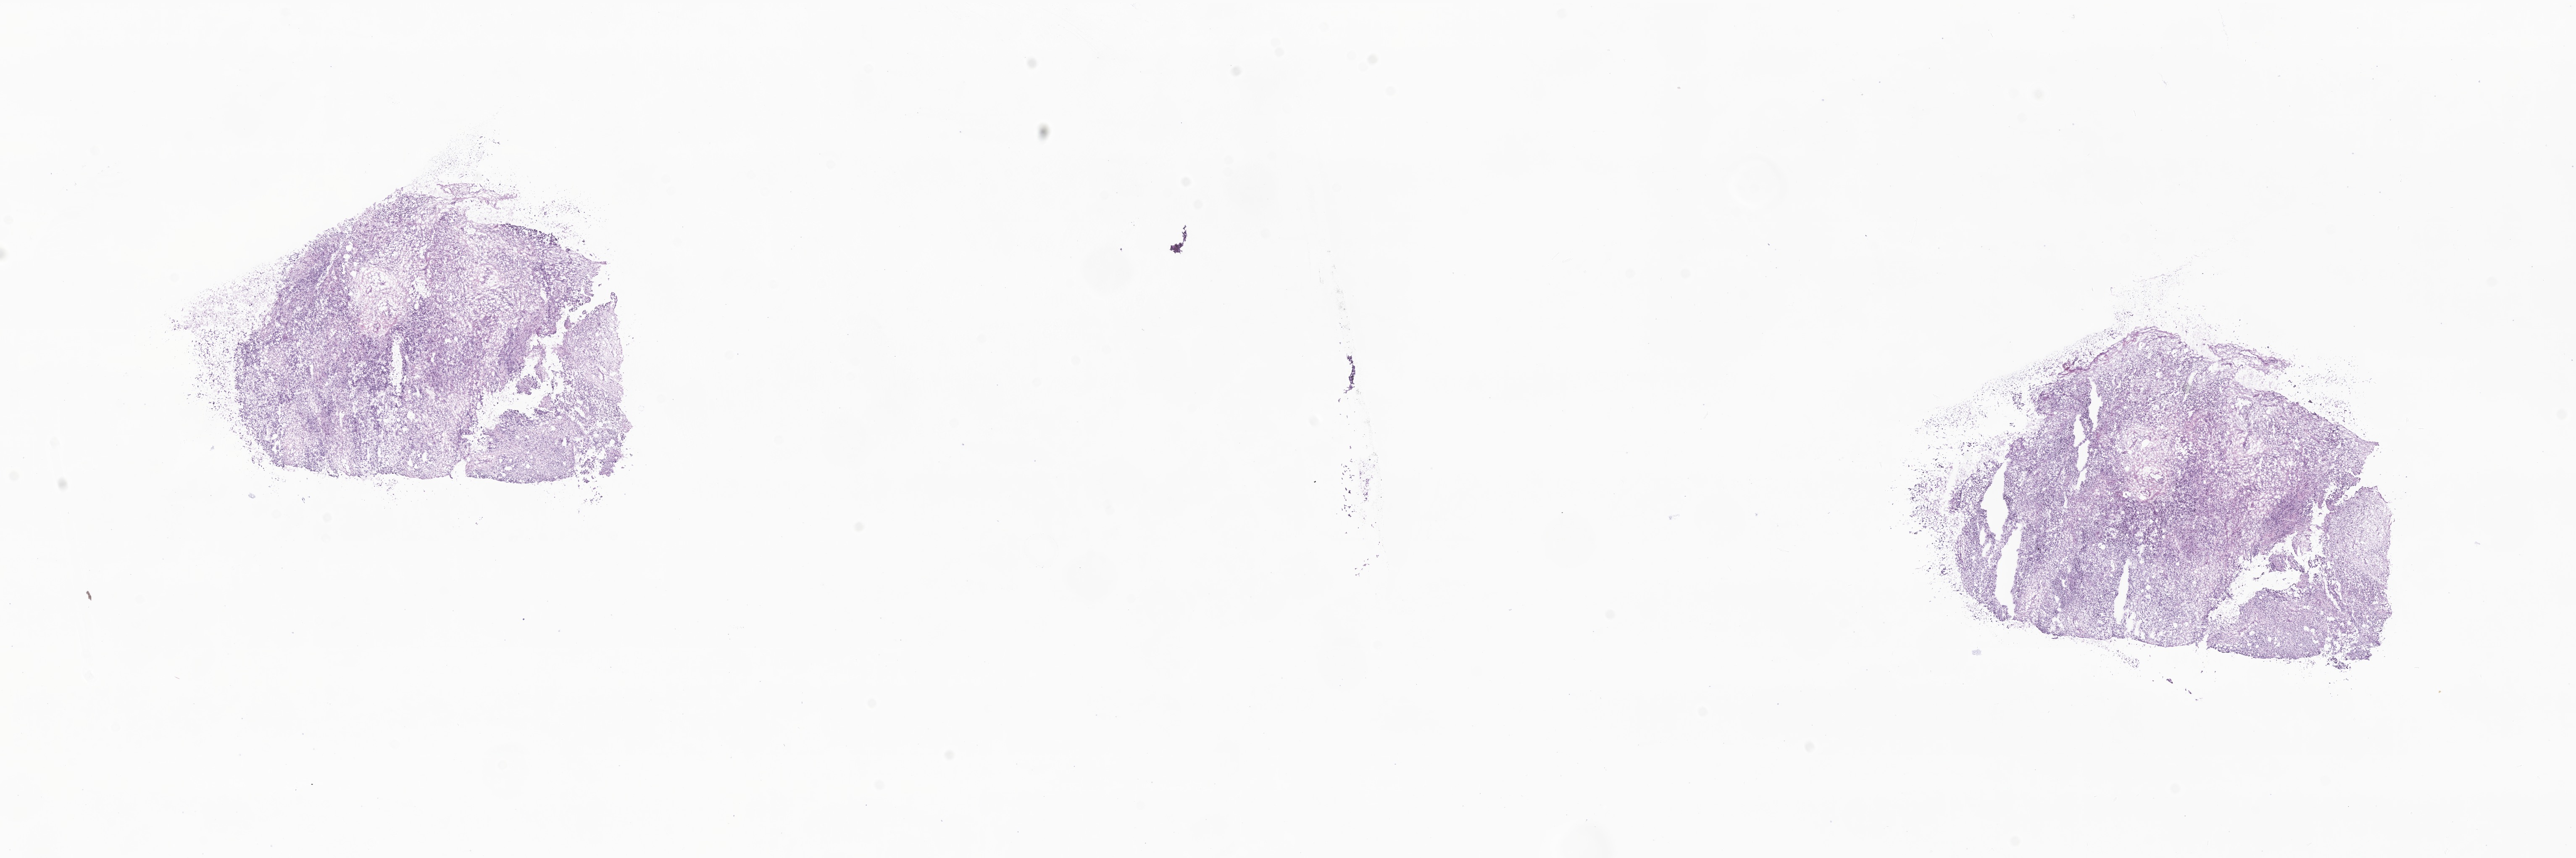
Digitized hematoxylin and eosin (H&E)-stained section of tumor tissue from the eye — shown as a low-resolution overview of the whole scanned area (about 25.8 x 8.6 mm), frozen section (OCT-embedded). Patient female; age 891 days (about 2.4 years).
Diagnosis (ICD-O-3 morphology term): Neoplasm, uncertain whether benign or malignant.